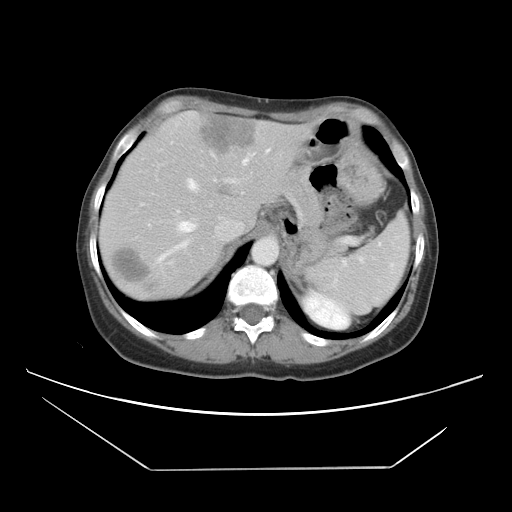
Contrast-enhanced abdominal CT, one axial slice. Slice 32 of 42 in the series (ordered by position). 120 kVp. Intravenous contrast given. Soft-tissue window (W 400 / L 40 HU). 512 × 512 image matrix, field of view 399 × 399 mm. Female patient, age 52 years. From the clinical record (not read from this slice): diagnosis: colorectal cancer liver metastases, imaged before liver resection; multiple liver metastases: yes; largest metastasis: 5.5 cm.
Annotated regions visible in this slice (expert manual segmentation):
- hepatic veins: bounding box (x1, y1, x2, y2) in pixels: (148, 148, 270, 264)
- liver: (101, 113, 310, 299)
- planned liver remnant (the part of the liver to remain after resection): (119, 121, 249, 225)
- portal vein (with intrahepatic branches): (140, 151, 241, 214)
- liver metastasis: (203, 120, 257, 154)
- liver metastasis: (114, 248, 150, 283)